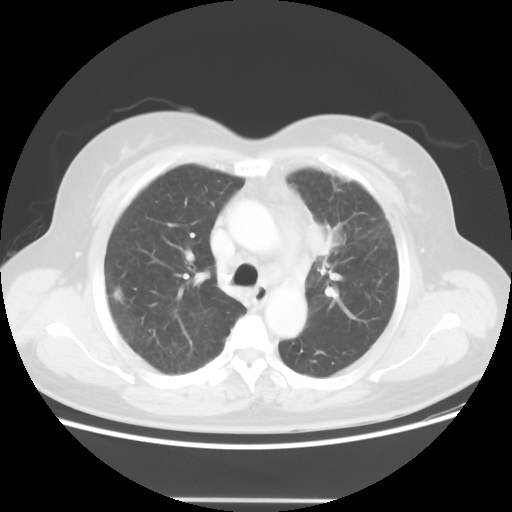
Chest CT, one axial slice. Slice 38 of 52 in the series (ordered by position). 120 kVp. Lung window (W 1500 / L -600 HU). 5 mm slice thickness. 512 × 512 image matrix. Female patient, age 52 years. From the clinical record (not read from this slice): clinical TNM (as recorded): T2 N3 M0.
Annotated regions visible in this slice (rectangle marked by the reading radiologist):
- lung tumour (recorded histology: adenocarcinoma): bounding box (x1, y1, x2, y2) in pixels: (300, 199, 348, 259)